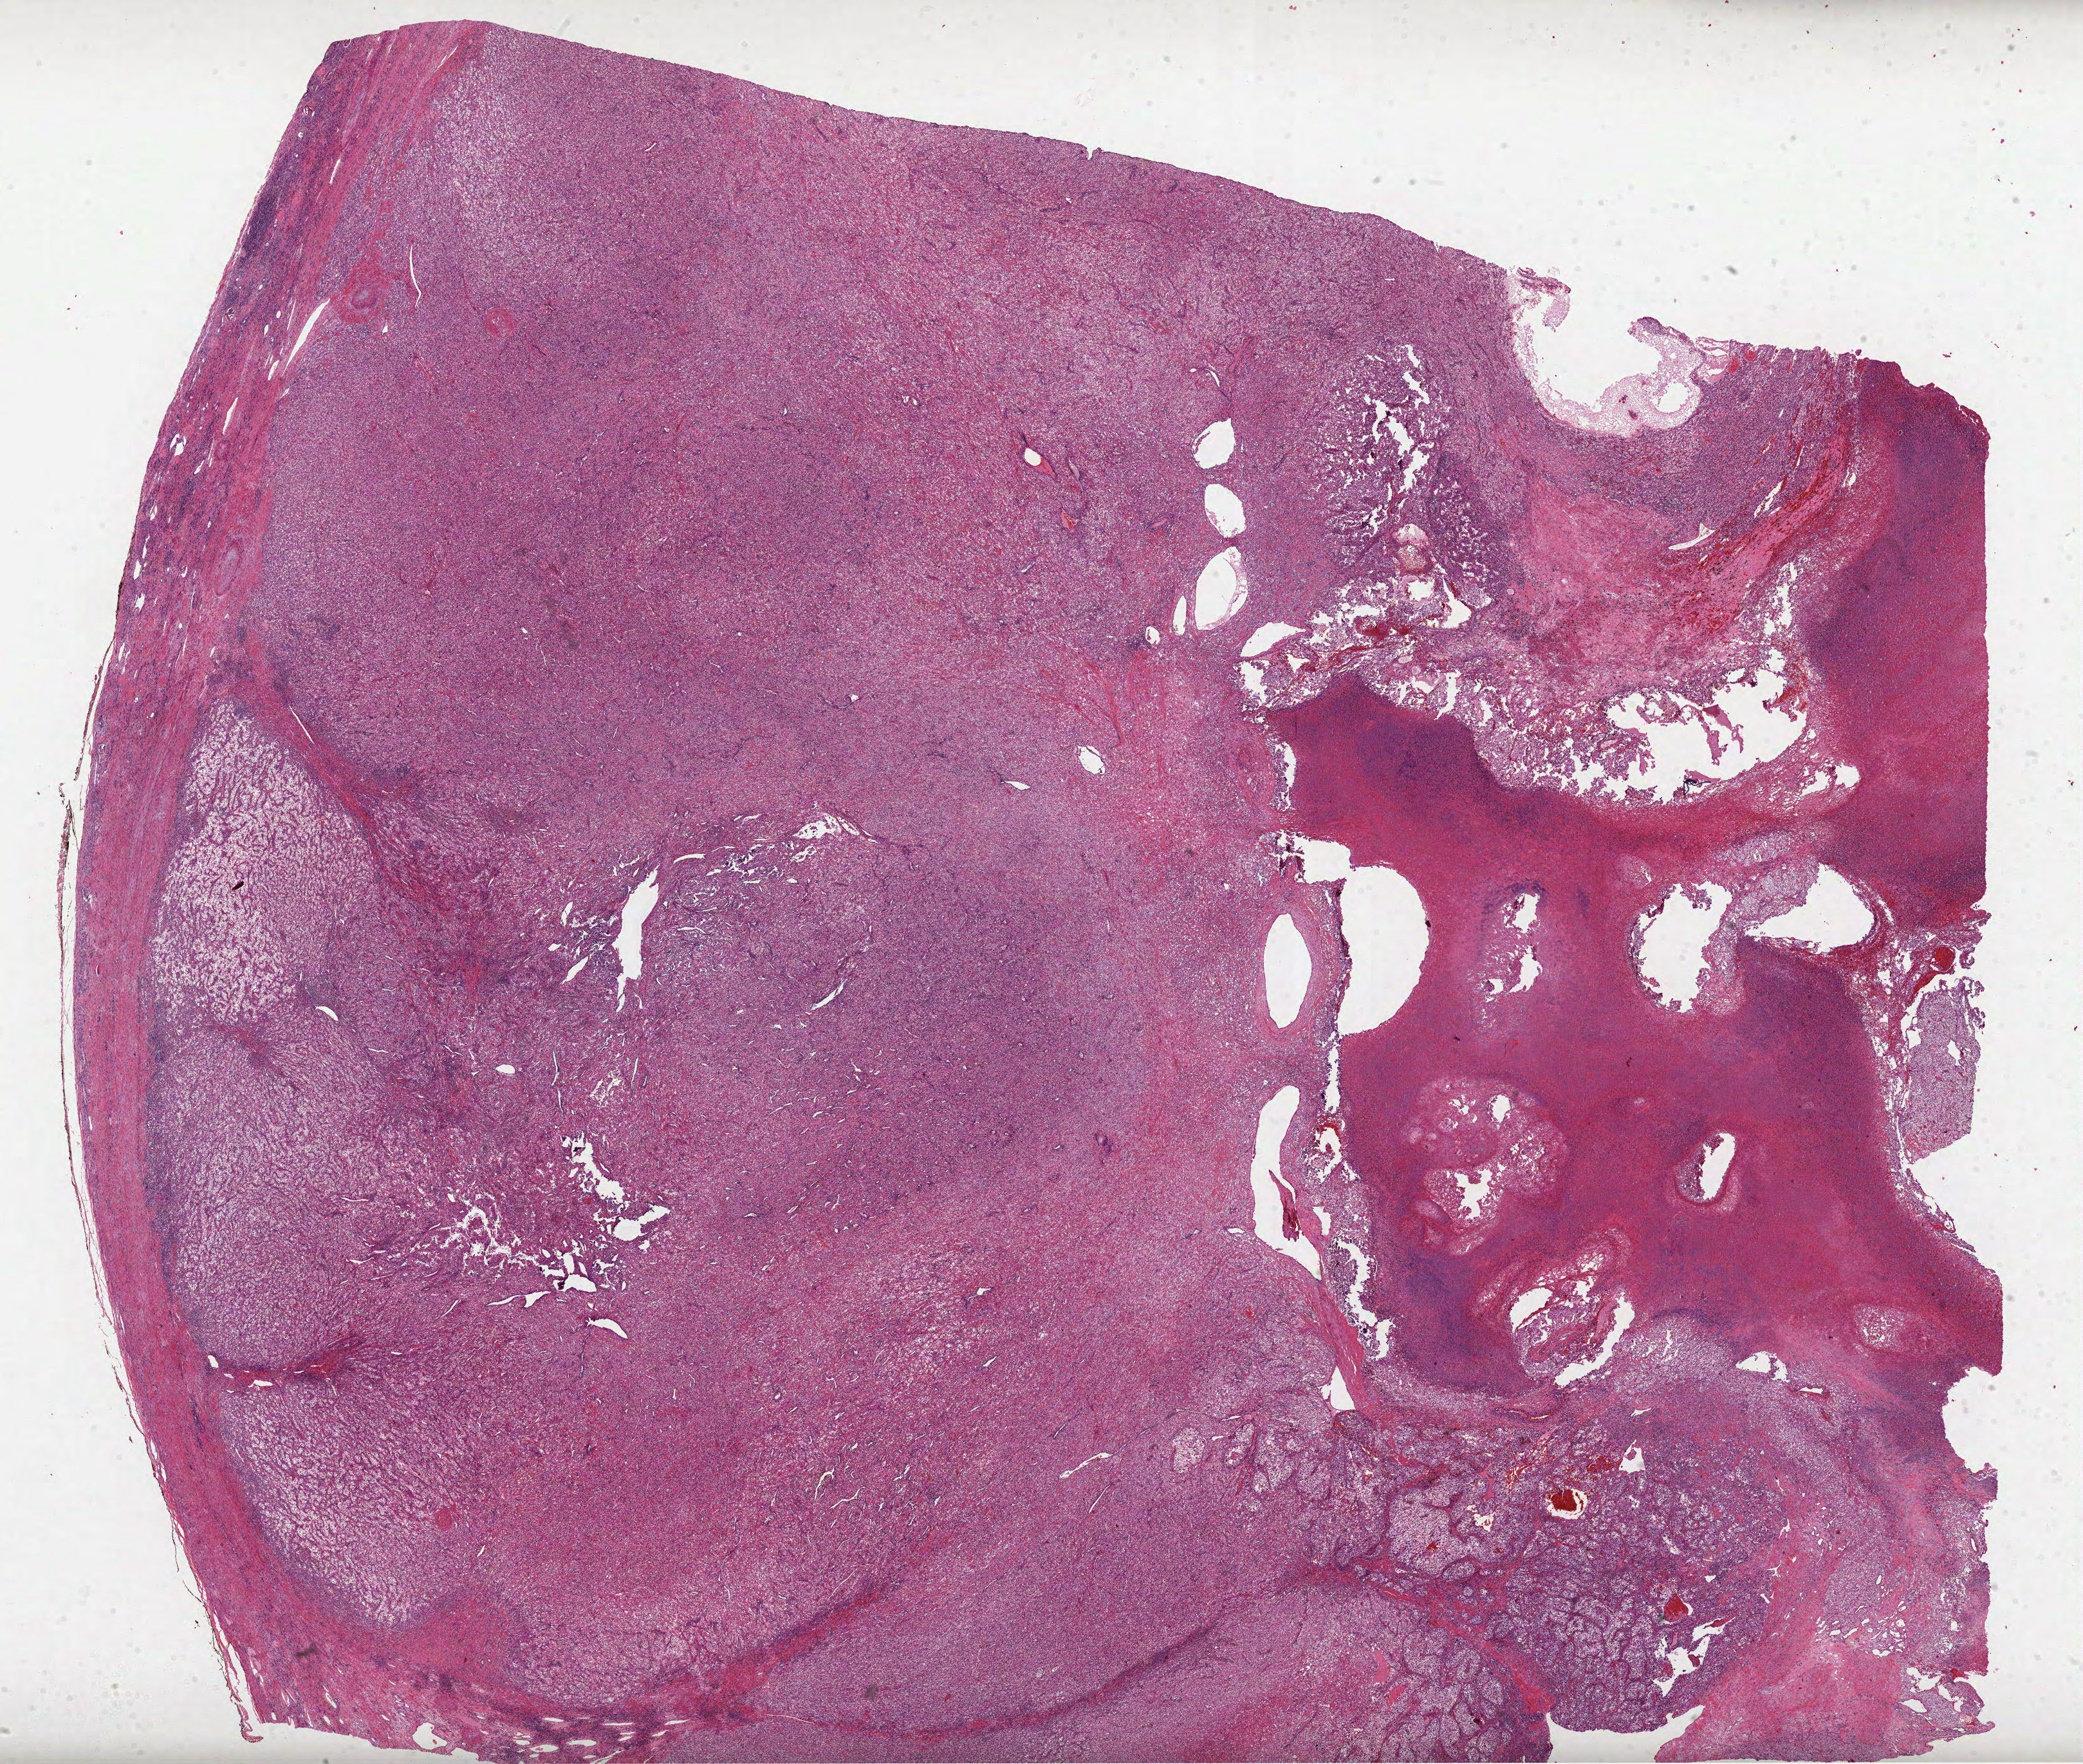
Hematoxylin and eosin (H&E) stained whole-slide image — shown as a low-resolution overview of the whole scanned area (about 26.1 x 22.1 mm, slide scanned at 40x); FFPE section; primary tumour sample from the kidney. Male patient; age at initial diagnosis 51 years. Histologic grade: G4 (undifferentiated).
Histologic diagnosis: Clear cell adenocarcinoma, NOS. AJCC pathologic stage: IV.